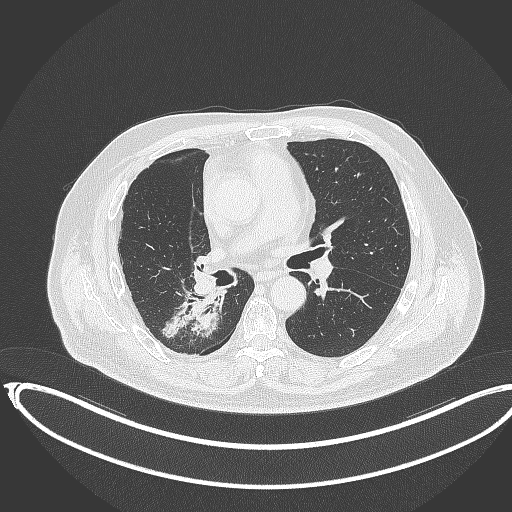
Chest CT, one axial slice; position 190 of 403 along the scan axis; reconstruction kernel B70f; lung window (W 1500 / L -600 HU); 1 mm slice thickness; 512 × 512 image matrix, field of view 436 × 436 mm. Patient: male, 68 years. From the clinical record (not read from this slice): clinical TNM (as recorded): T2a N0 M0.
Annotated regions visible in this slice (rectangle marked by the reading radiologist):
- lung tumour (recorded histology: adenocarcinoma): bounding box (x1, y1, x2, y2) in pixels: (161, 286, 224, 338)